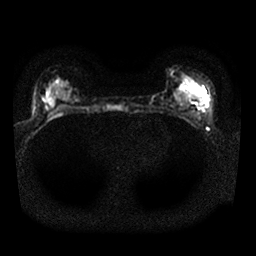
Breast MRI, one axial slice; slice 11 of 25 in the series (ordered by position); diffusion-weighted series; image 2 of 4 stored at this slice position (different b-values; order by instance number); 1.5 T; 4 mm slice thickness; 256 × 256 image matrix, field of view 320 × 320 mm. Female patient.
Structures marked on this image (expert manual segmentation):
- tumour on diffusion-weighted imaging: box from (x=198, y=91) to (x=206, y=109) px